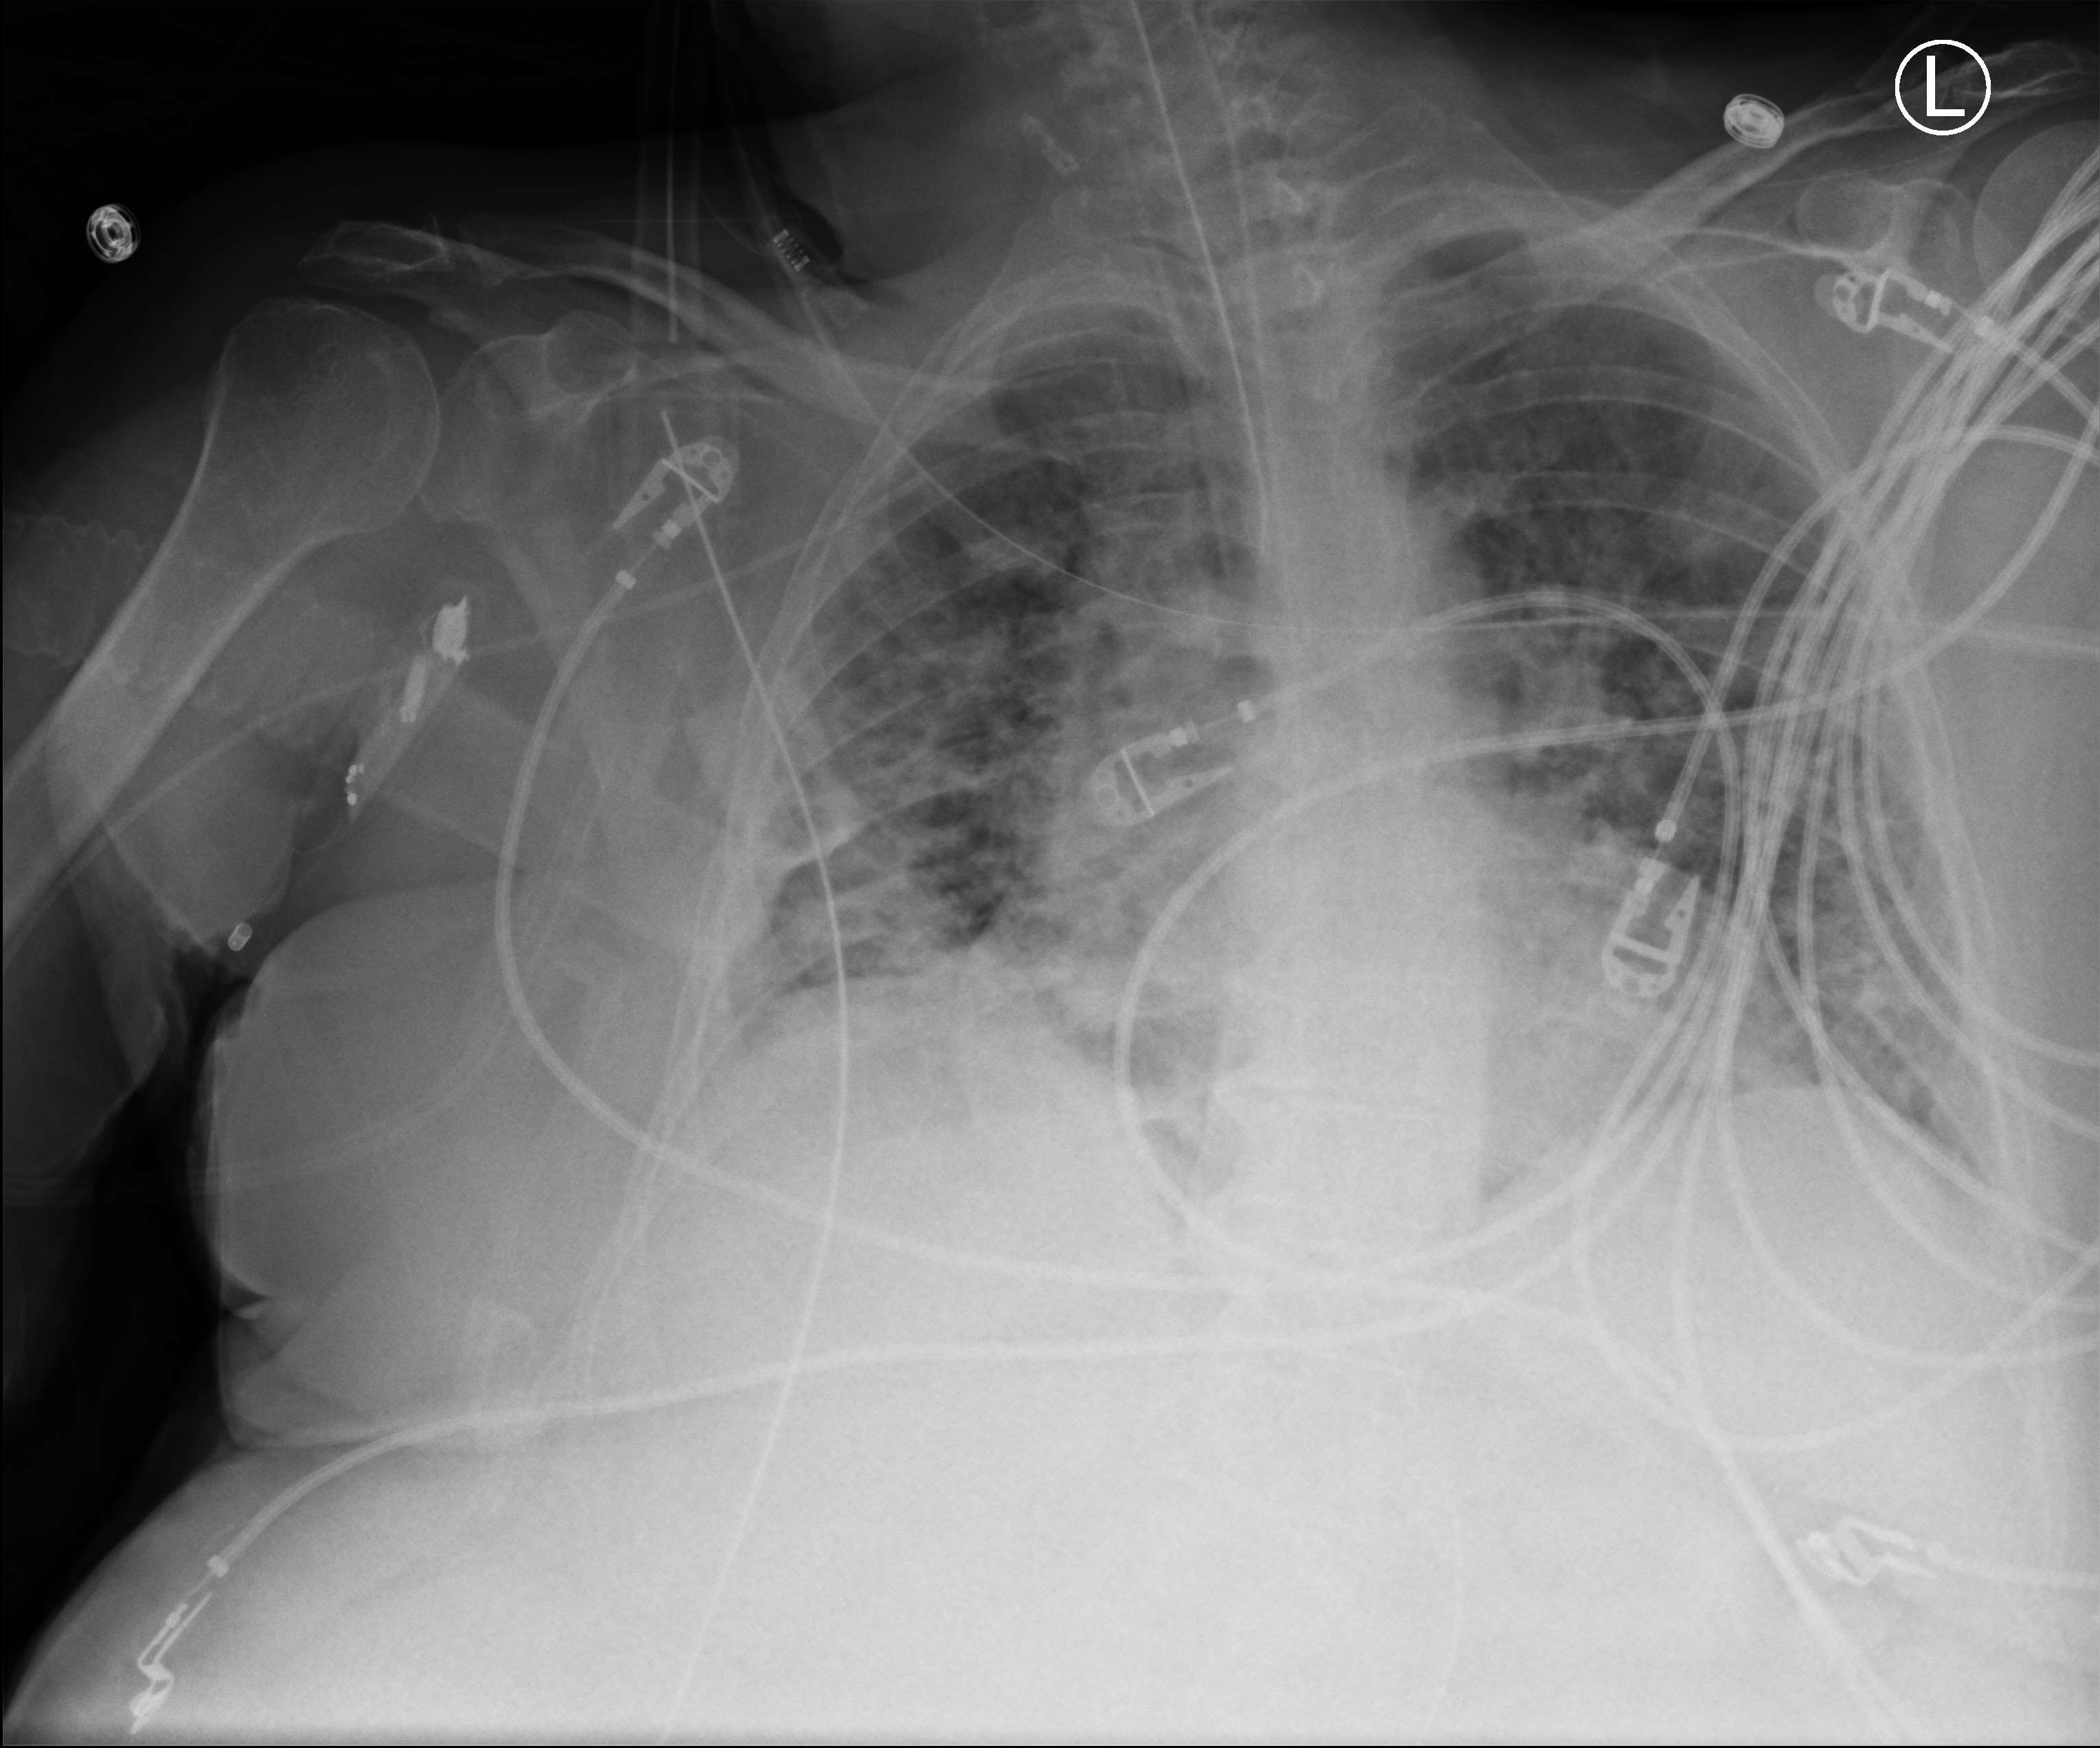
Bedside chest radiograph (computed radiography), anteroposterior (AP) projection. Female patient hospitalised with COVID-19, age 75–90 years.
Admission-level facts for this patient (not findings on this image; timing relative to this image not recorded): chronic kidney disease (admission record): no; COPD (admission record): yes.